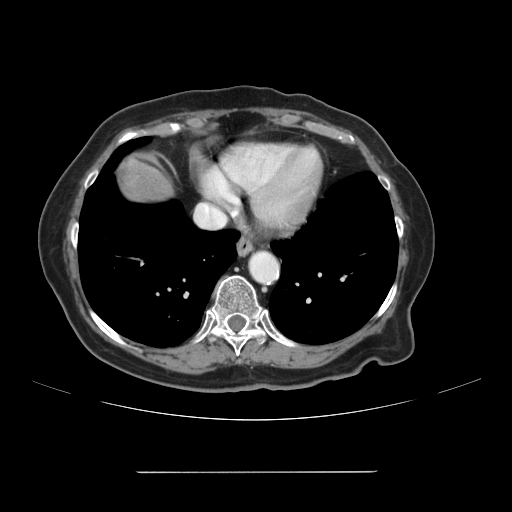
Contrast-enhanced abdominal CT, one axial slice. Slice 107 of 111 in the series (ordered by position). Soft-tissue window (W 400 / L 40 HU). 512 × 512 image matrix, field of view 400 × 400 mm. Female patient, age 74 years. Case-level facts recorded for this patient, not image findings: diagnosis: colorectal cancer liver metastases, imaged before liver resection; multiple liver metastases: yes; largest metastasis: 1.1 cm; disease in both lobes: yes.
Annotated regions visible in this slice (manually delineated by an expert):
- liver: bounding box (x1, y1, x2, y2) in pixels: (117, 155, 173, 204)